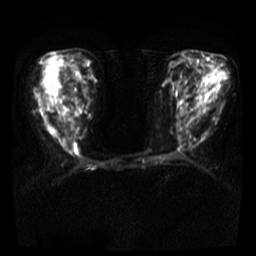
Breast MRI, one axial slice; slice 14 of 36 in the series (ordered by position); diffusion-weighted series; image 2 of 4 stored at this slice position (different b-values; order by instance number); 3 T; 5 mm slice thickness; 256 × 256 image matrix. Female patient.
Outlined on this slice (manually delineated by an expert):
- tumour on diffusion-weighted imaging: bounding box [x1, y1, x2, y2] px = [61, 140, 68, 151]